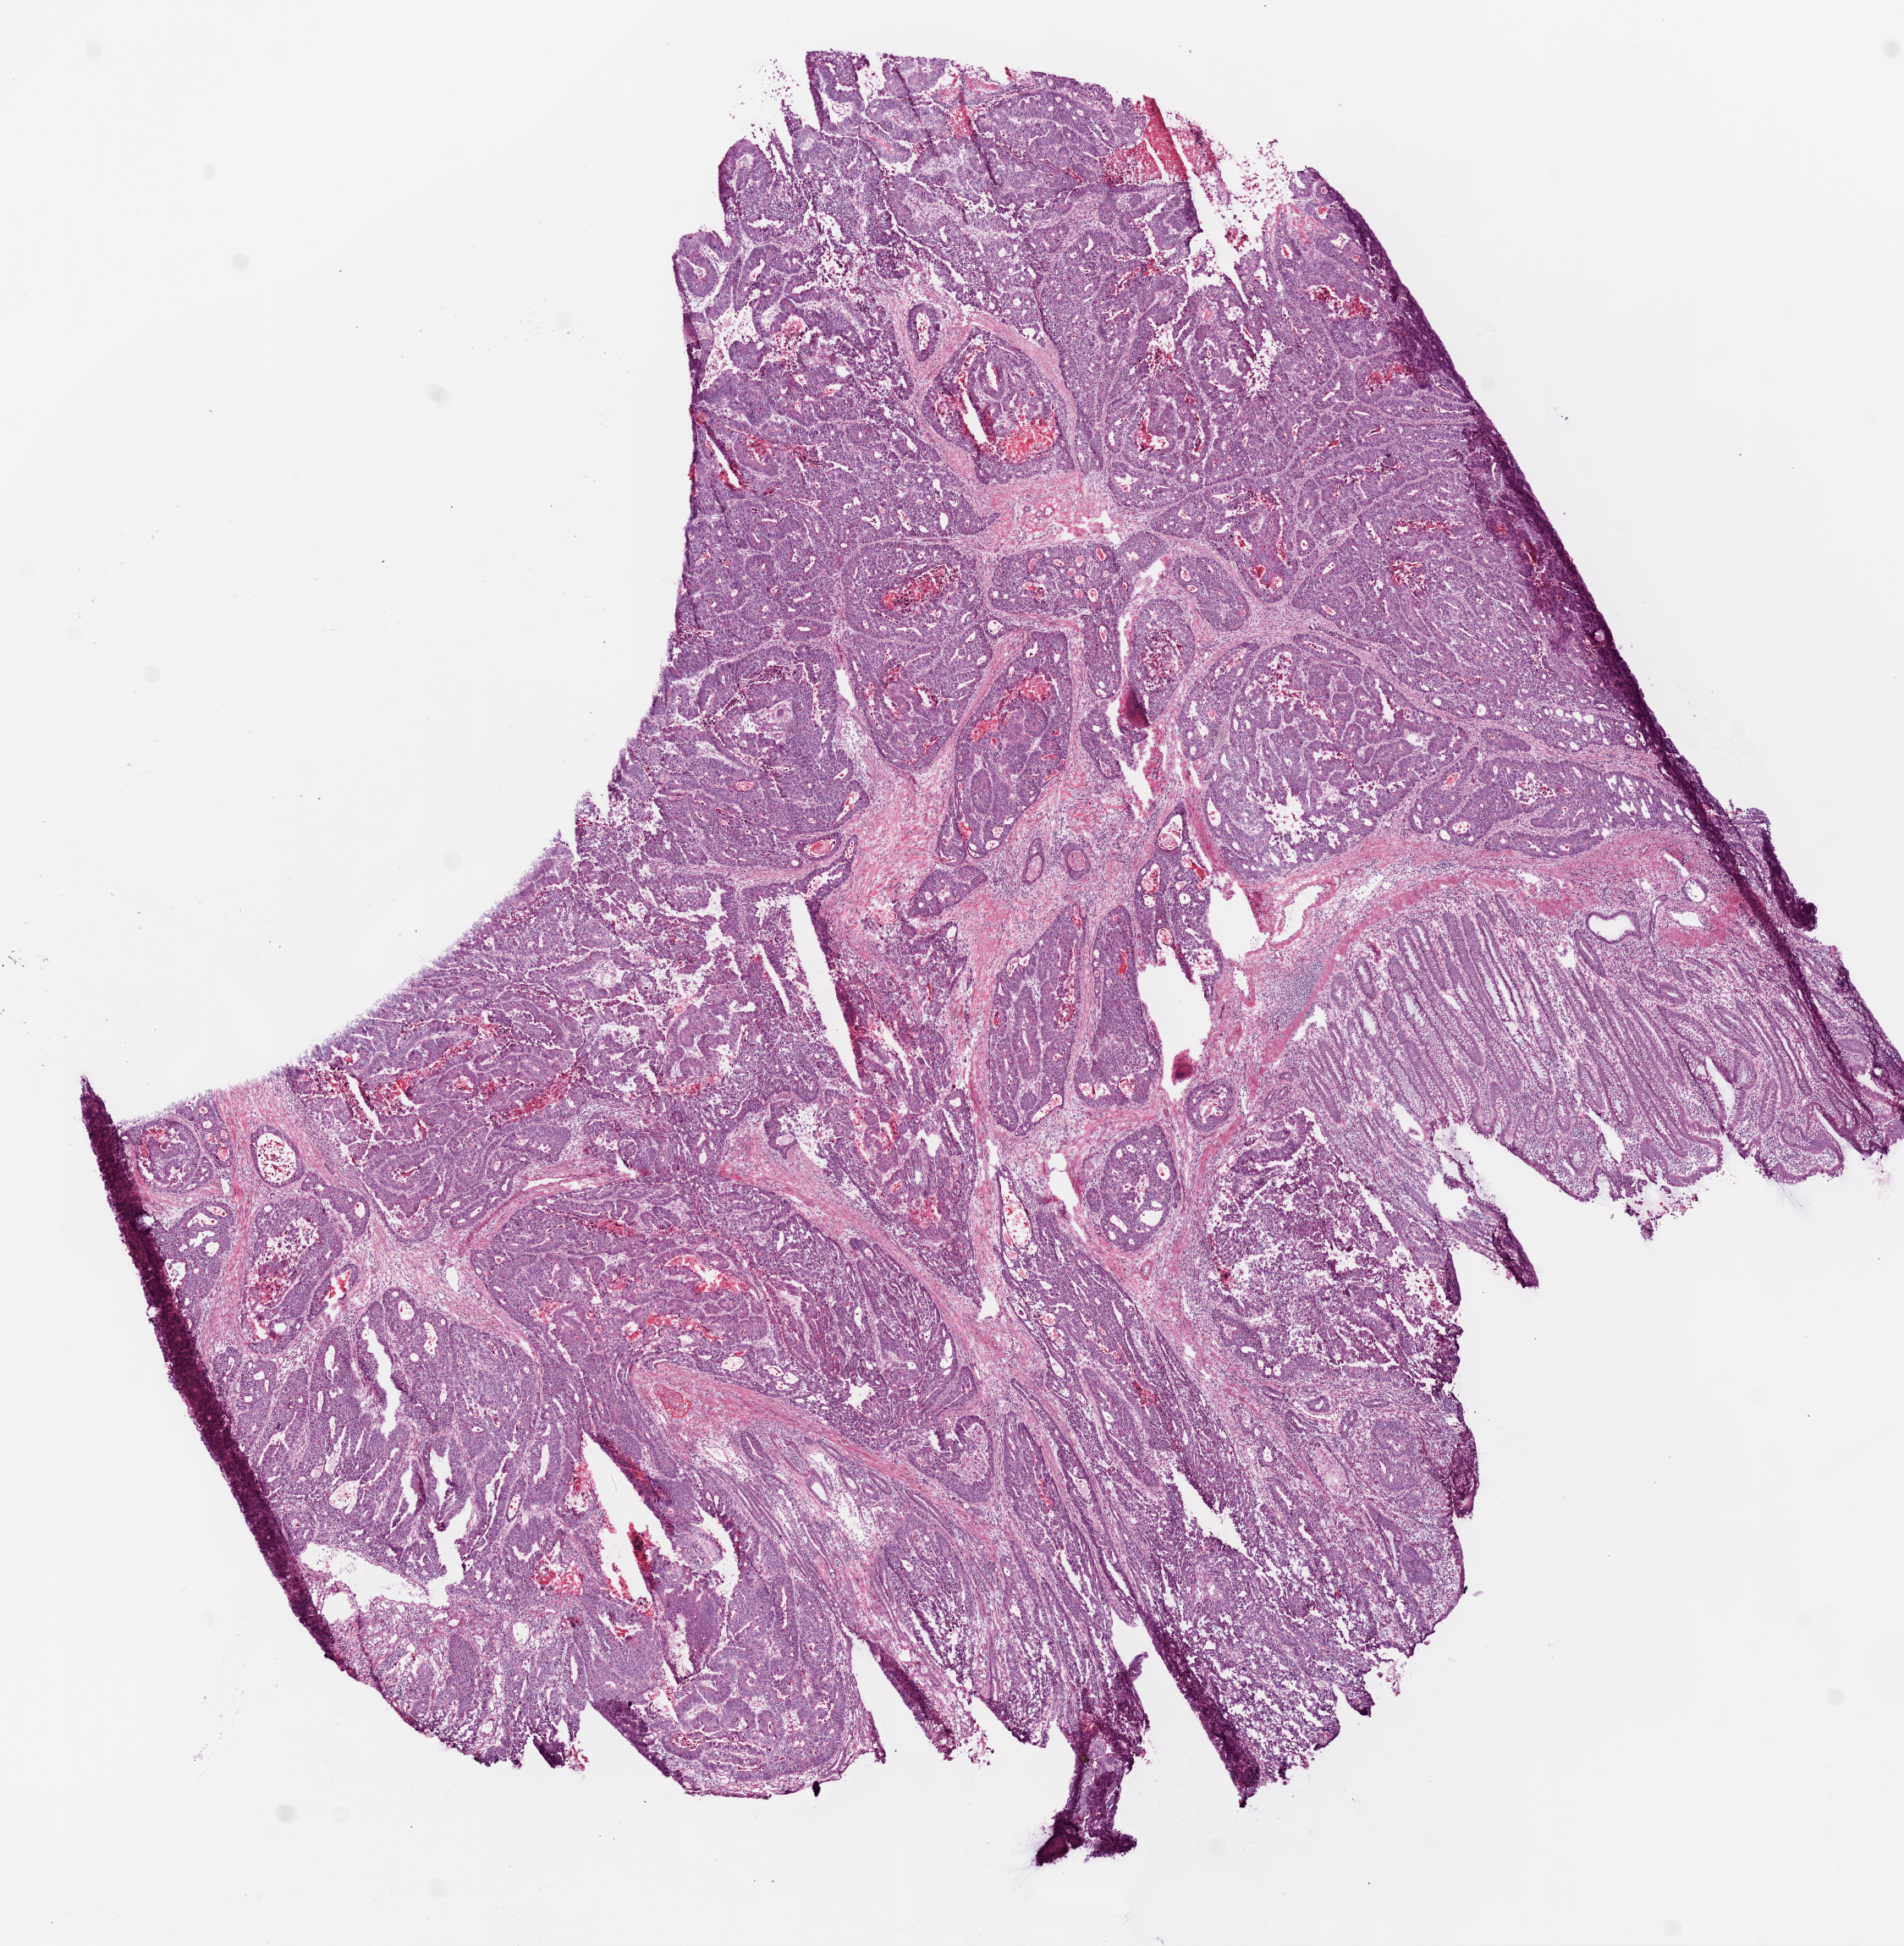
H&E-stained whole-slide image, a low-resolution overview of the entire scanned area, about 9.0 x 9.2 mm; frozen section from the bottom of the tissue portion; colon, primary tumour sample. Patient: male, age at initial diagnosis 60 years. Slide review estimates, as recorded: tumour cells 90%, tumour nuclei 95%, normal cells 0%, stromal cells 10%, necrosis 0%.
* AJCC pathologic stage: IIA
* lymph nodes positive (case pathology): 0 of 54 examined
* histologic diagnosis: Adenocarcinoma, NOS